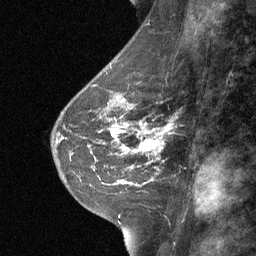
Breast MRI (dynamic contrast-enhanced), one sagittal slice. Slice 29 of 64 in the series (ordered by position). Dynamic contrast-enhanced study with each time point stored as its own series, time point 2 of 3 at this slice position (early post-contrast, ordered by acquisition time). 1.5 T. TE 4.8 ms, TR 27 ms. 2 mm slice thickness. 256 × 256 image matrix, field of view 180 × 180 mm. Patient: female, 42 years. Case-level facts recorded for this patient, not image findings: setting: breast cancer imaged before/during neoadjuvant chemotherapy; receptor status: triple-negative.
Annotated regions visible in this slice (semi-automatic segmentation, software-assisted and operator-edited):
- analysis volume of interest (the breast-tissue region the enhancement analysis was run in; not a lesion): bounding box <99,117,174,187> (left, top, right, bottom; pixels)
- tumour enhancement mask (voxels above the 90 % enhancement threshold inside the analysis volume of interest): <122,125,170,156>